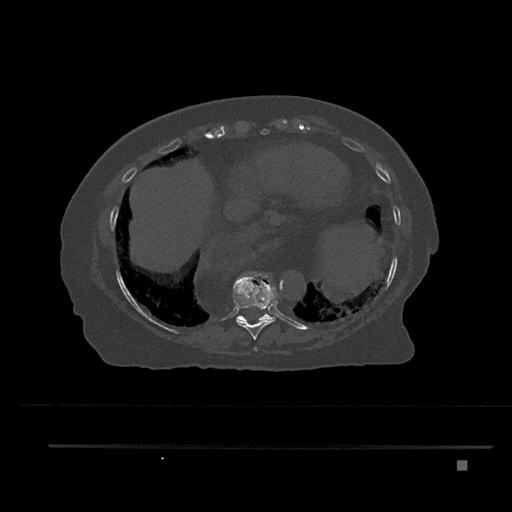
CT including the spine, one axial slice. Position 385 of 797 along the scan axis. Bone window (W 1800 / L 400 HU). 512 × 512 image matrix, field of view 437 × 437 mm. Female patient, age 76 years. From the clinical record (not read from this slice): primary cancer: lung.
Structures marked on this image (semi-automatic segmentation, software-assisted and operator-edited):
- T10 vertebra: bounding box [x1, y1, x2, y2] px = [236, 314, 275, 322]
- T8 vertebra: [253, 347, 258, 351]
- T9 vertebra: [233, 272, 277, 340]